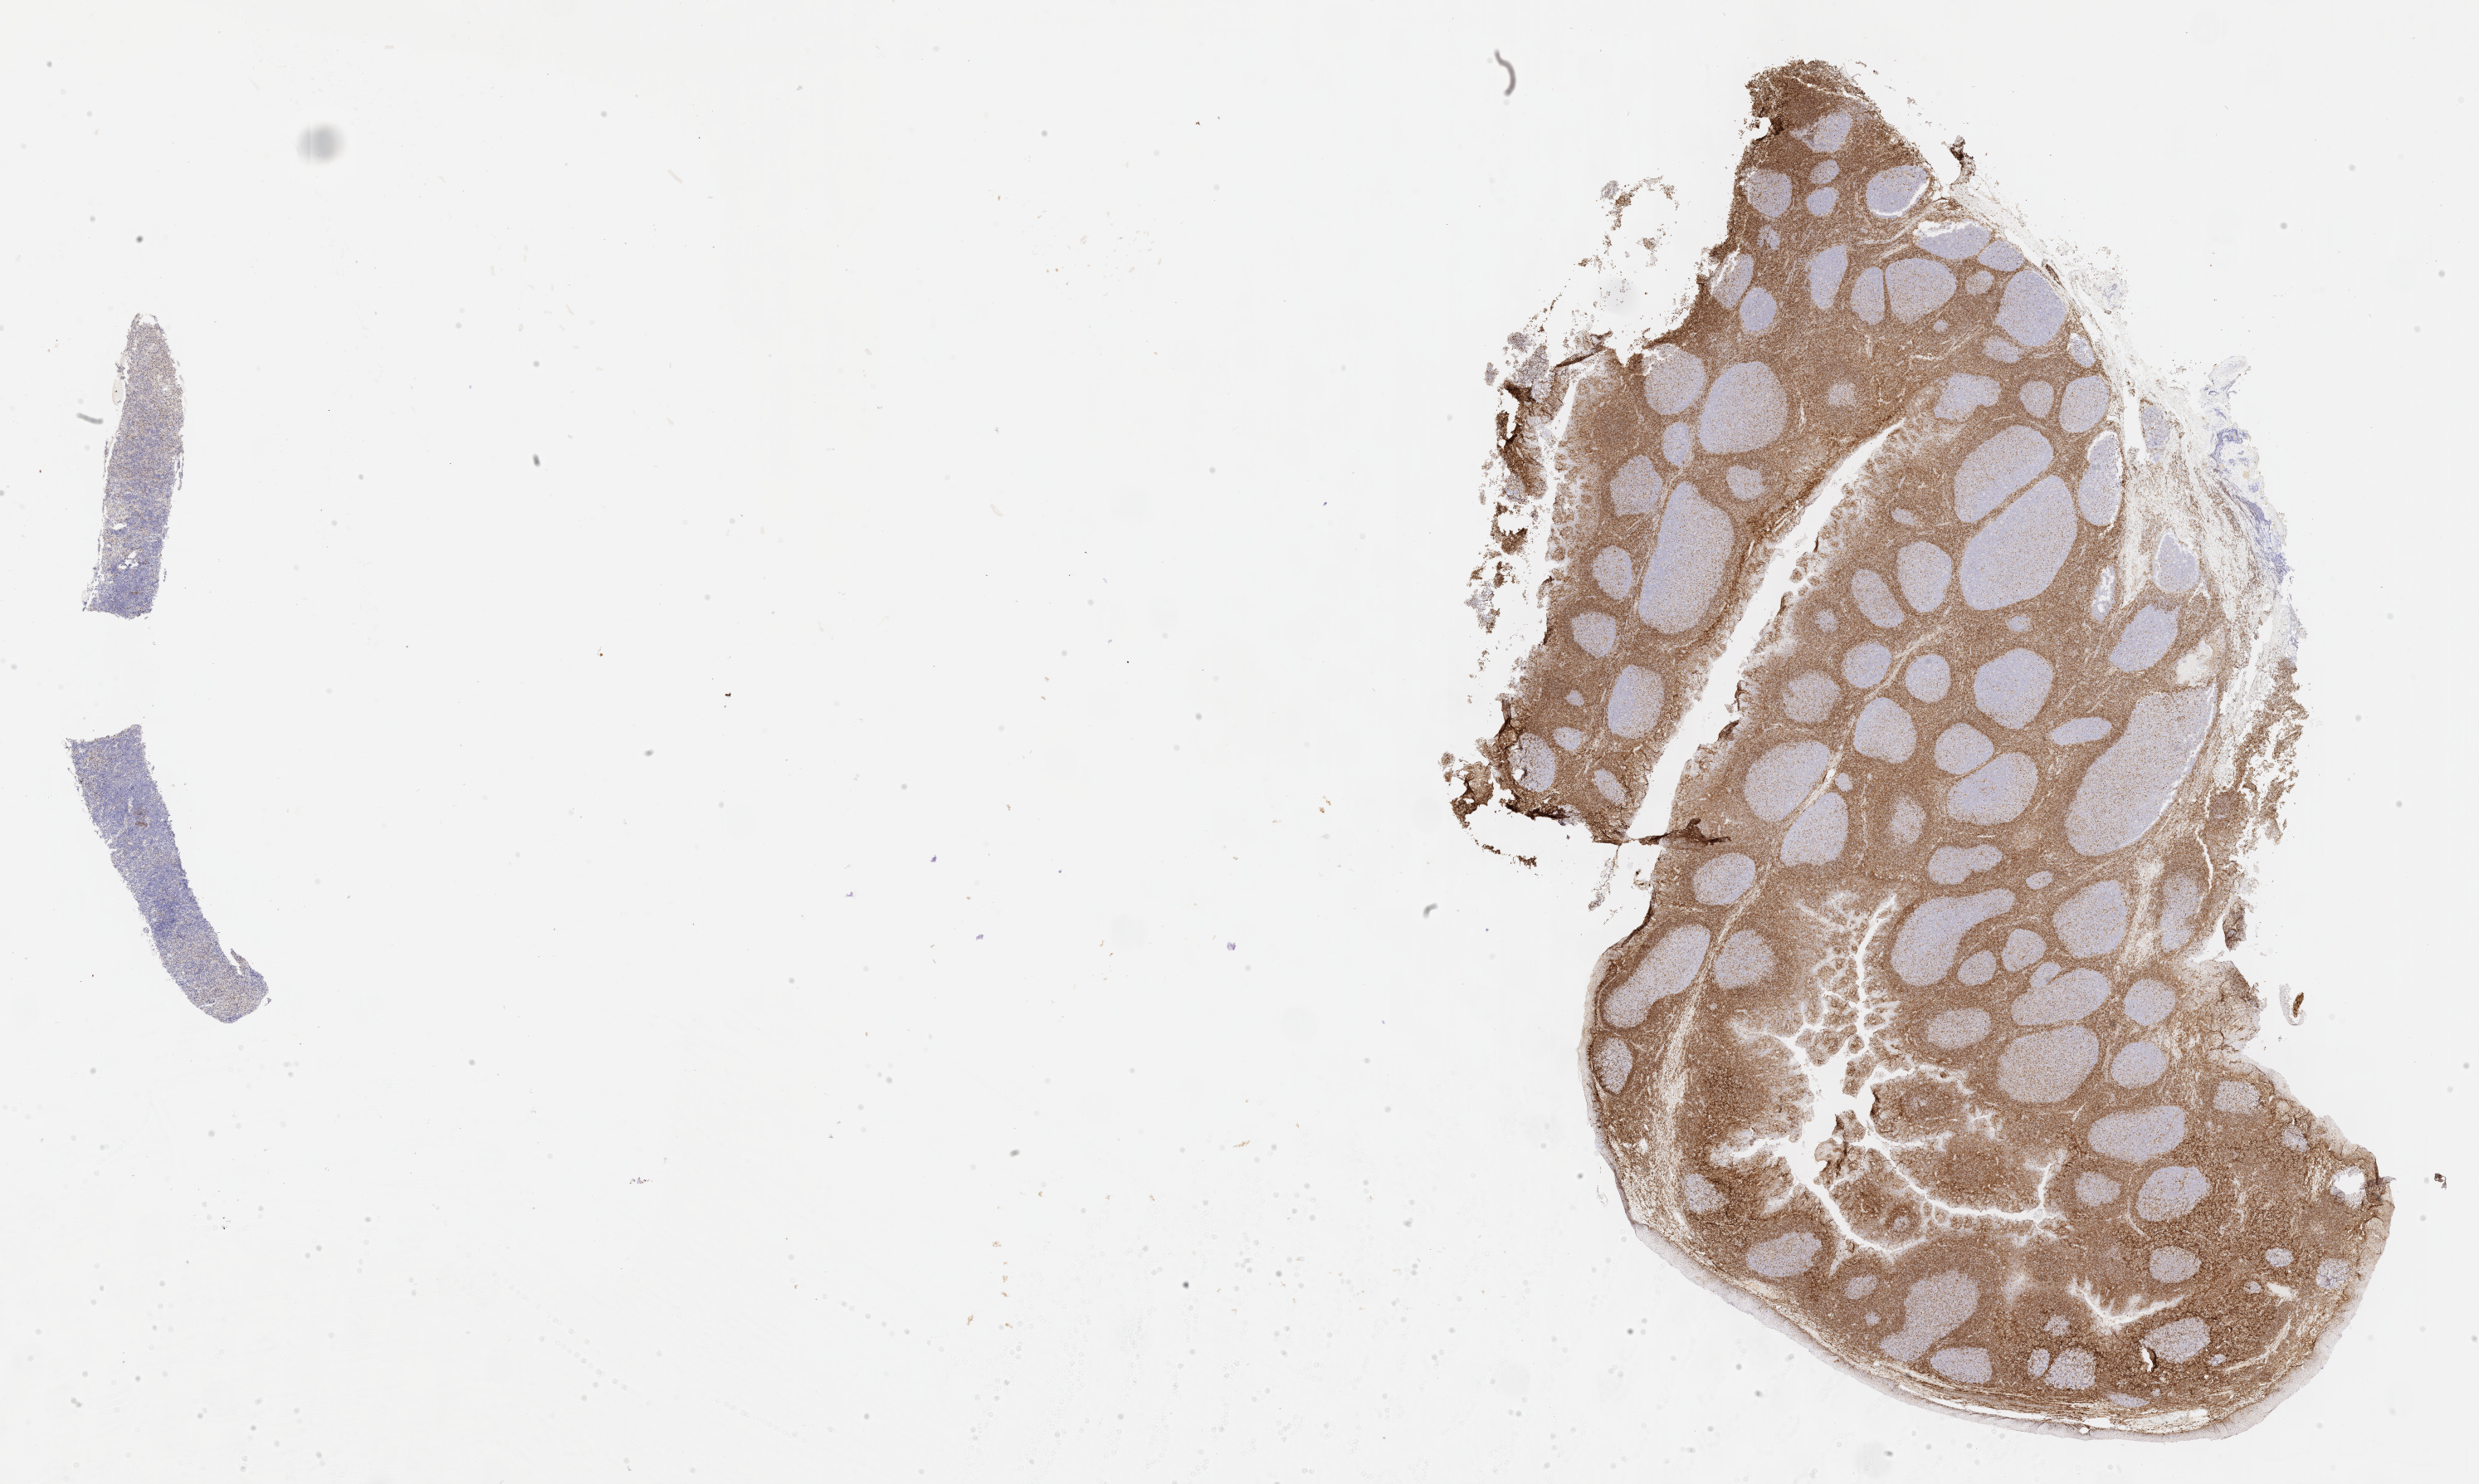
IHC for BCL2, whole-slide image, low-resolution overview of the scanned area, about 24.2 x 14.5 mm. Patient sex: male.
- specimen: tumor tissue